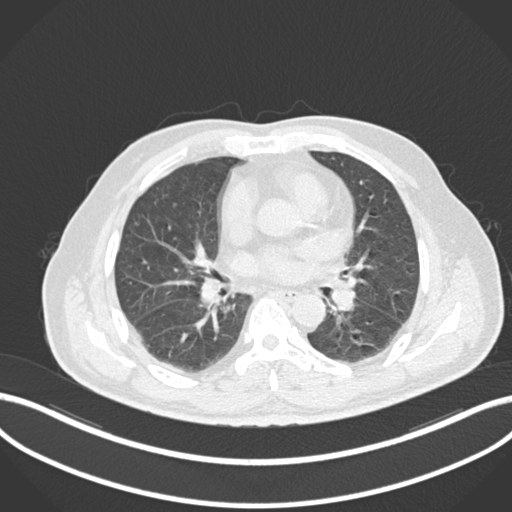
Chest CT, one axial slice. Slice 69 of 161 in the series (ordered by position). 120 kVp. Lung window (W 1500 / L -600 HU). 512 × 512 image matrix, field of view 400 × 400 mm. Patient: male, 71 years. From the clinical record (not read from this slice): clinical TNM (as recorded): T1b N0 M0.
Structures marked on this image (rectangle marked by the reading radiologist):
- lung tumour (recorded histology: squamous cell carcinoma): box from (x=327, y=280) to (x=359, y=315) px